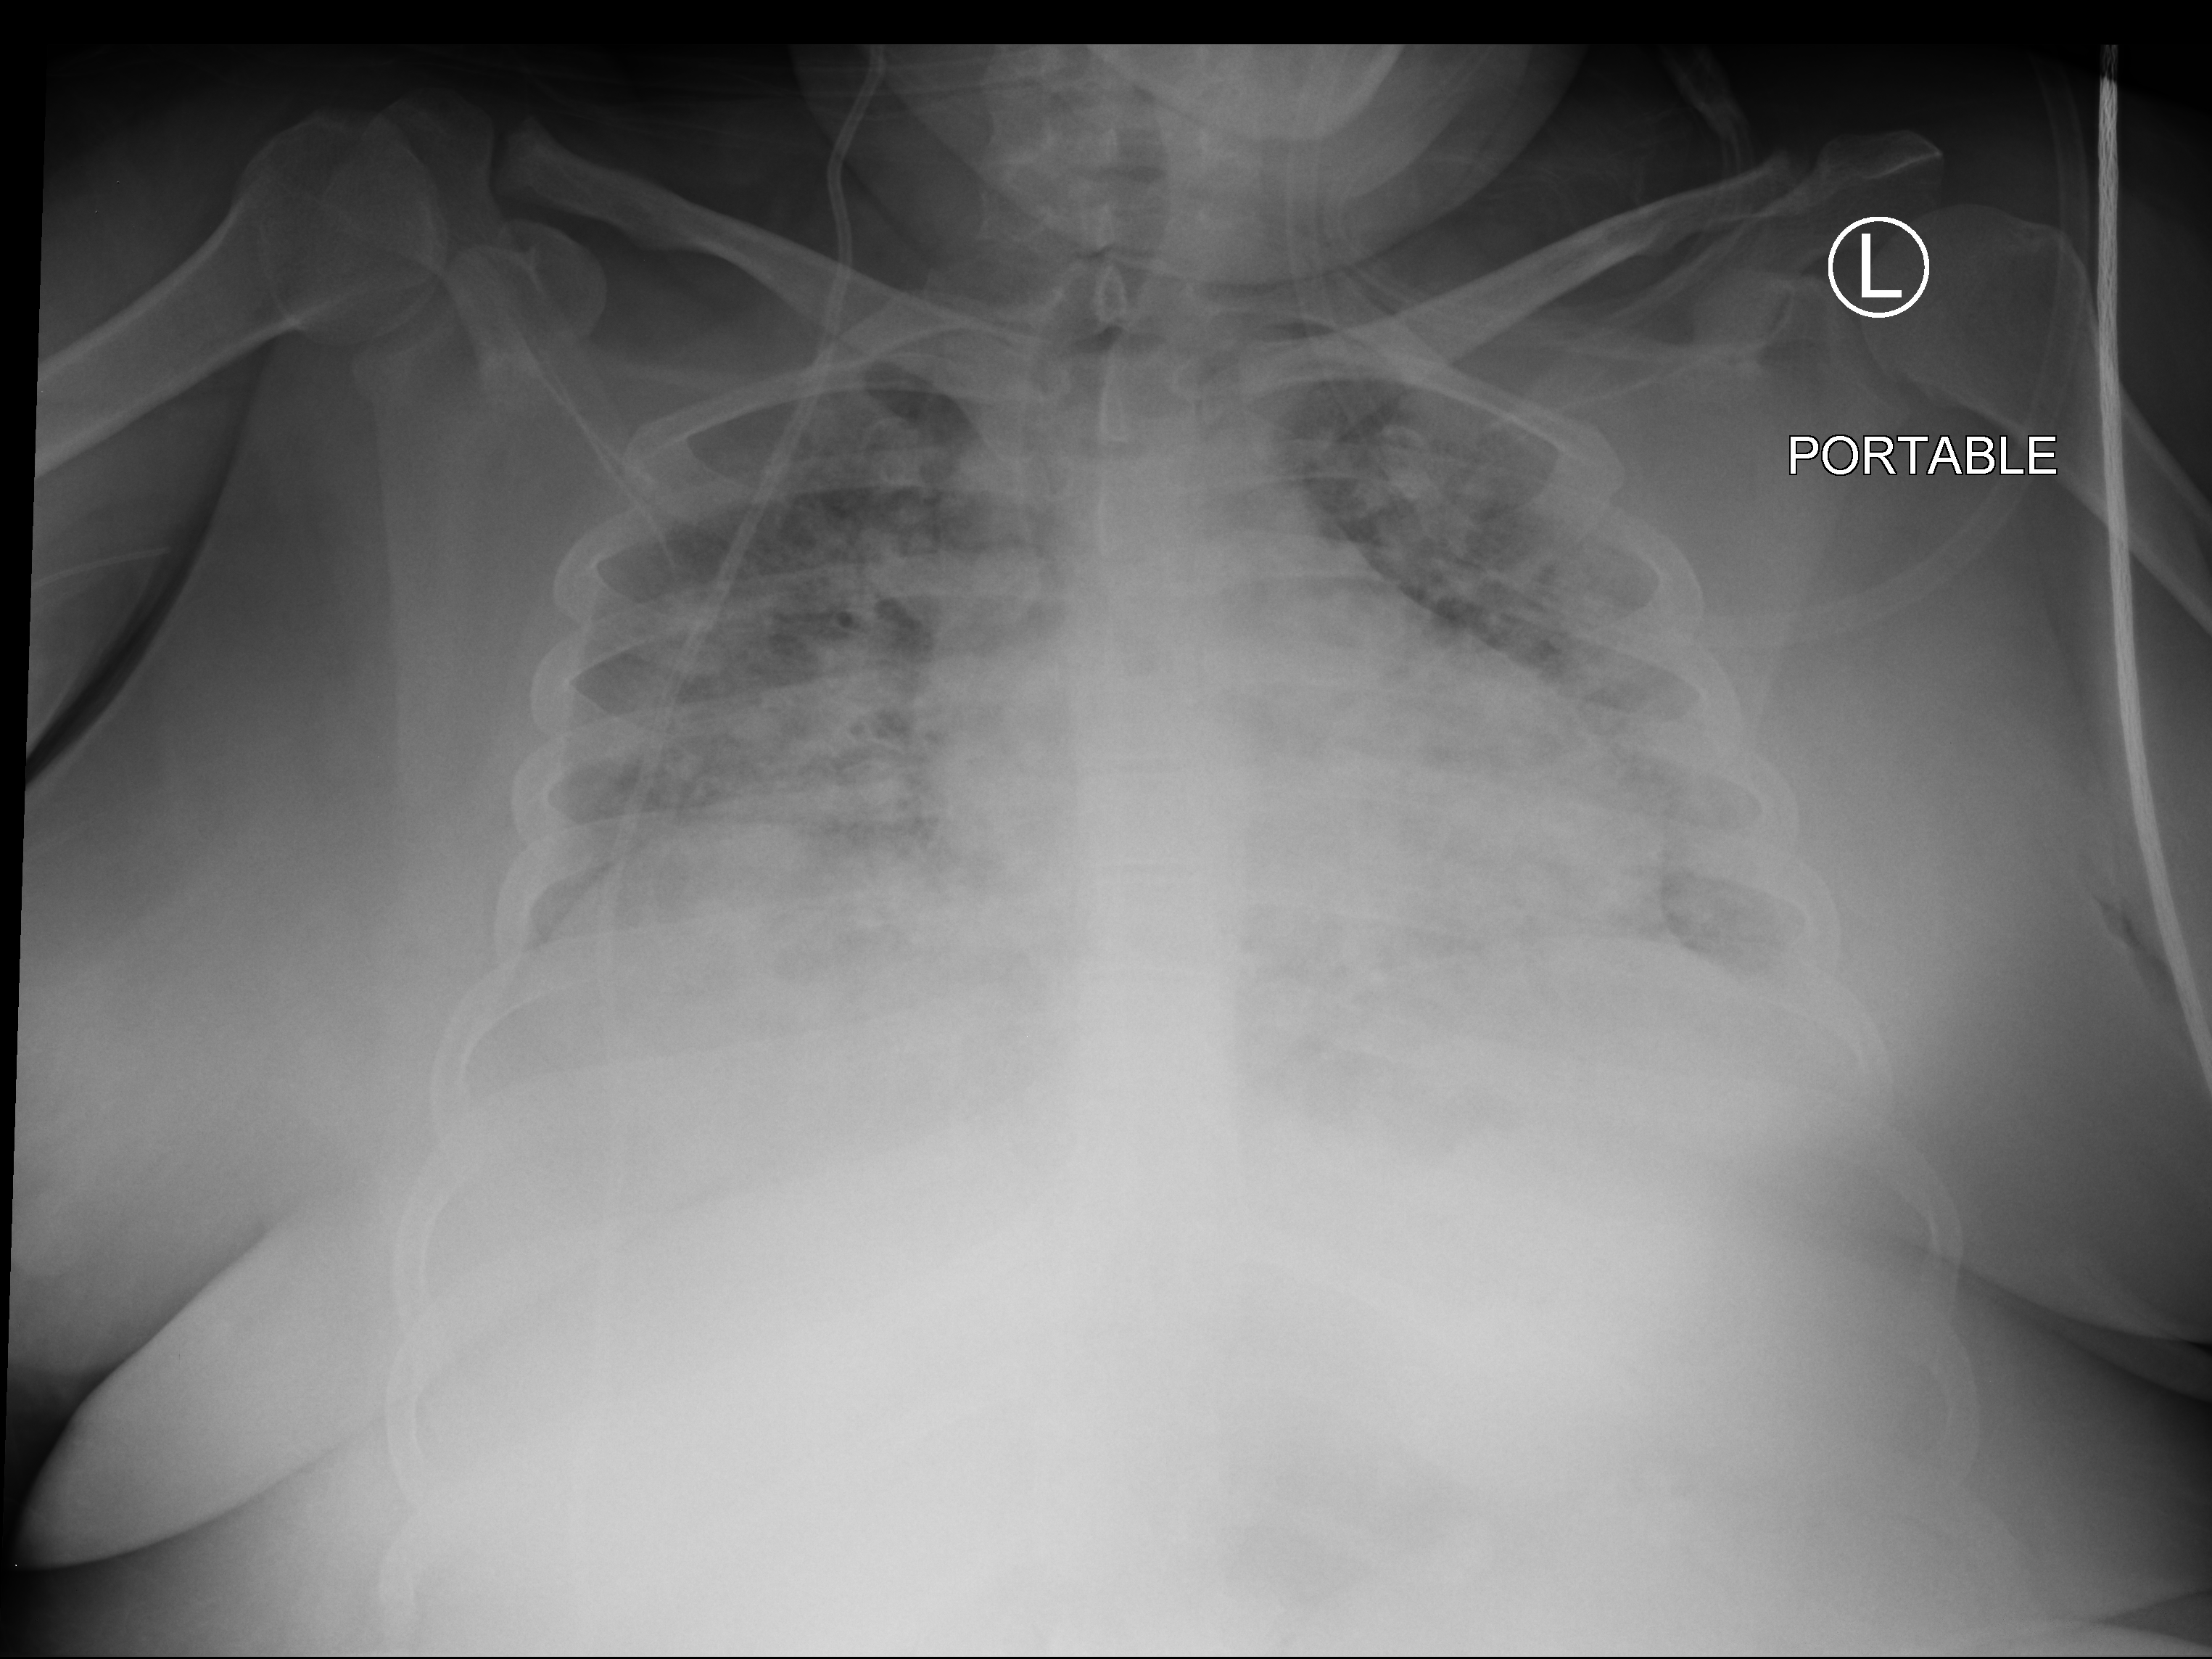
Portable chest radiograph; anteroposterior (AP) projection. Female patient hospitalised with COVID-19, age 18–59 years.
From the hospital-stay record, not from the radiograph (when in the stay this image was taken is not recorded): mechanically ventilated during this hospital stay: no; admitted to intensive care during this hospital stay: no; length of hospital stay: 9 days.